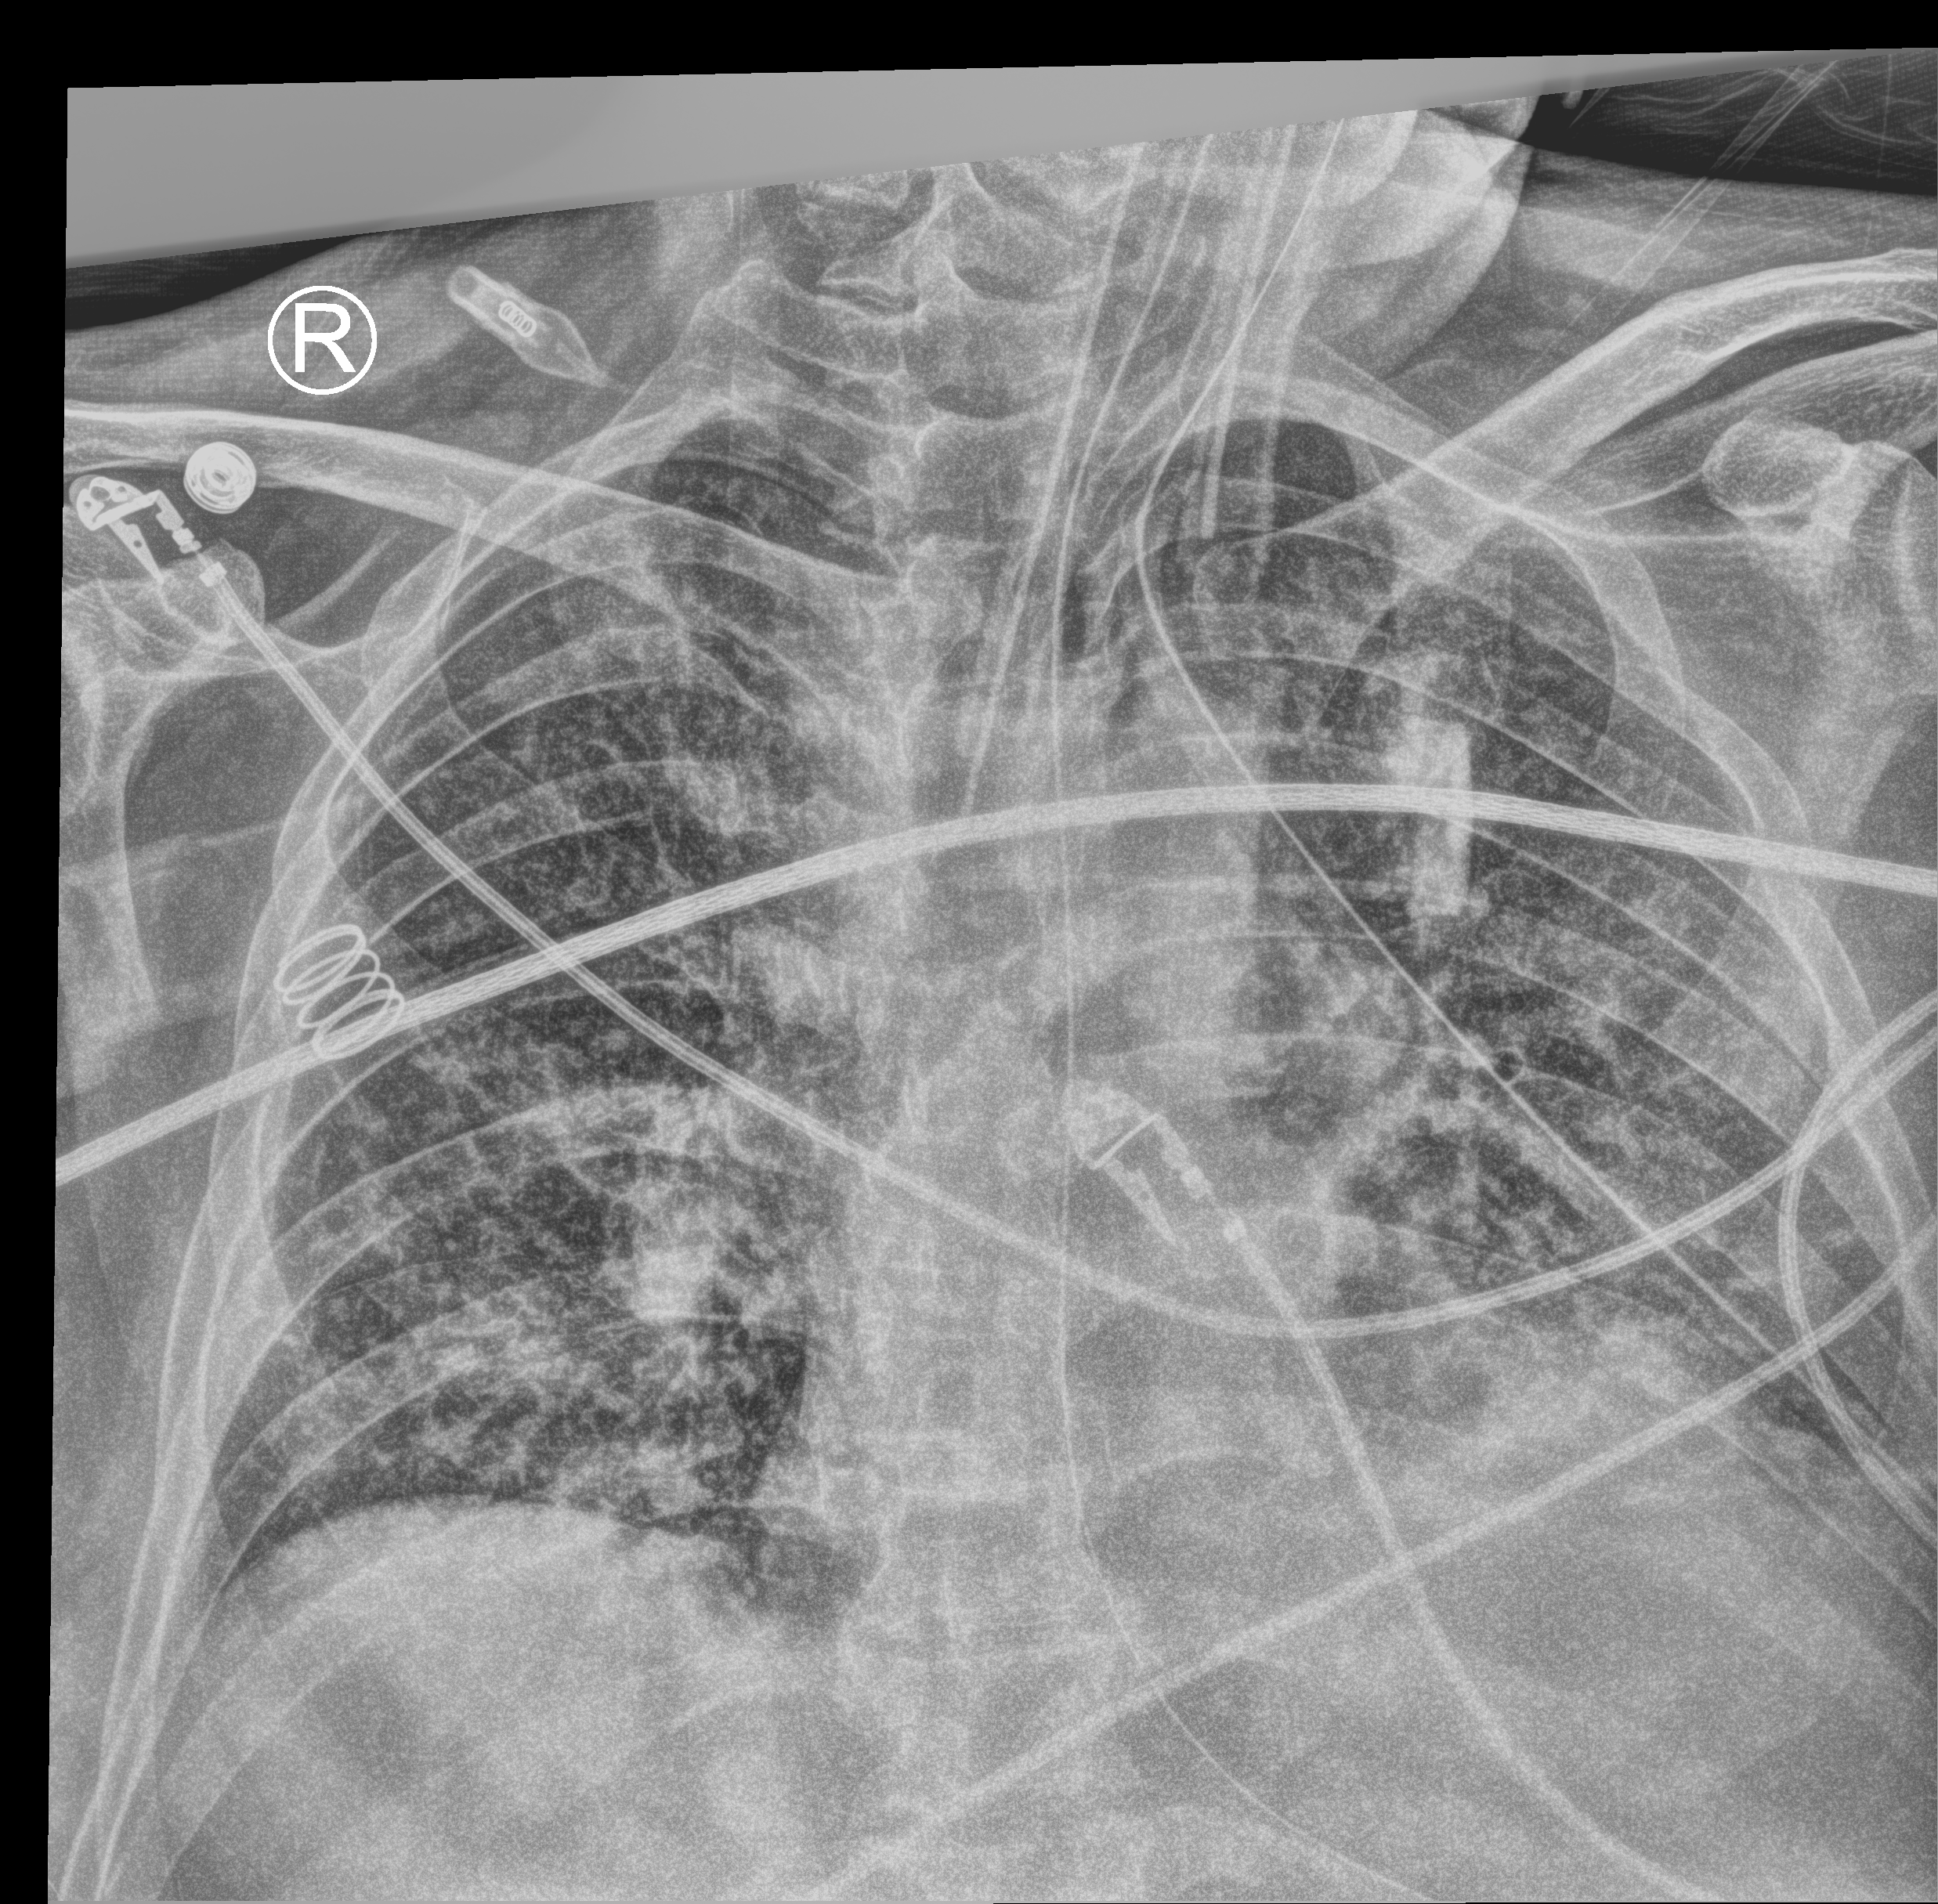
Chest X-ray (portable). Male patient hospitalised with COVID-19, age 18–59 years.
Admission-level facts for this patient (not findings on this image; timing relative to this image not recorded):
- length of hospital stay: 19 days
- diabetes (admission record): no
- COPD (admission record): no